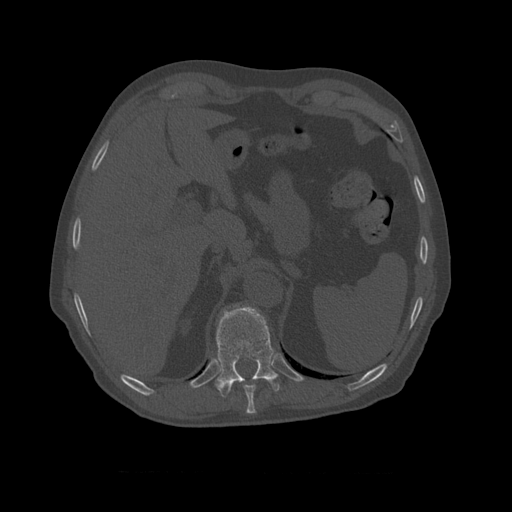
CT including the spine, one axial slice. Slice 407 of 450 in the series (ordered by position). Reconstruction kernel STANDARD. 120 kVp. Bone window (W 1800 / L 400 HU). 512 × 512 image matrix, field of view 405 × 405 mm. Patient age 75 years. Case-level facts recorded for this patient, not image findings: primary cancer: prostate.
Annotated regions visible in this slice (semi-automatic segmentation, software-assisted and operator-edited):
- T10 vertebra: bounding box [x1, y1, x2, y2] px = [215, 306, 280, 398]
- T9 vertebra: [243, 385, 256, 411]